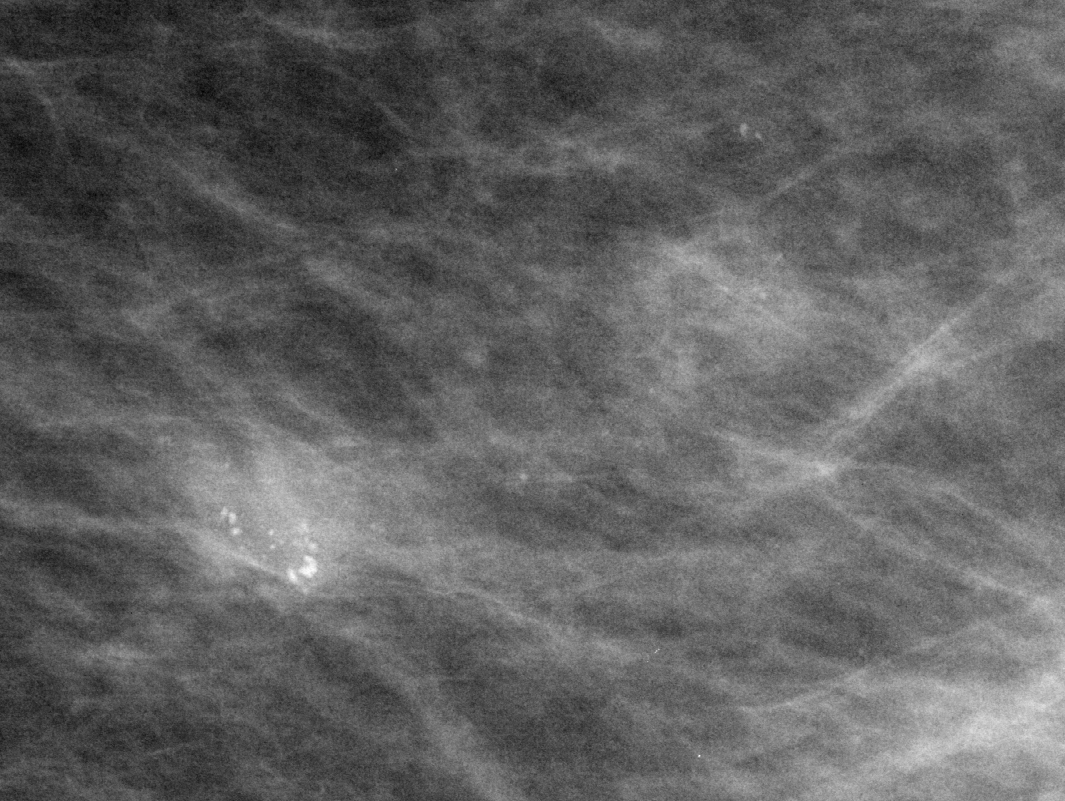
Region of interest cut from a scanned film mammogram (one marked finding); left breast; MLO view.
Marked abnormality: calcifications, morphology pleomorphic, distribution clustered; BI-RADS assessment category 4; subtlety rating 4 on a 1 (subtle) to 5 (obvious) scale; pathology (as recorded): malignant.